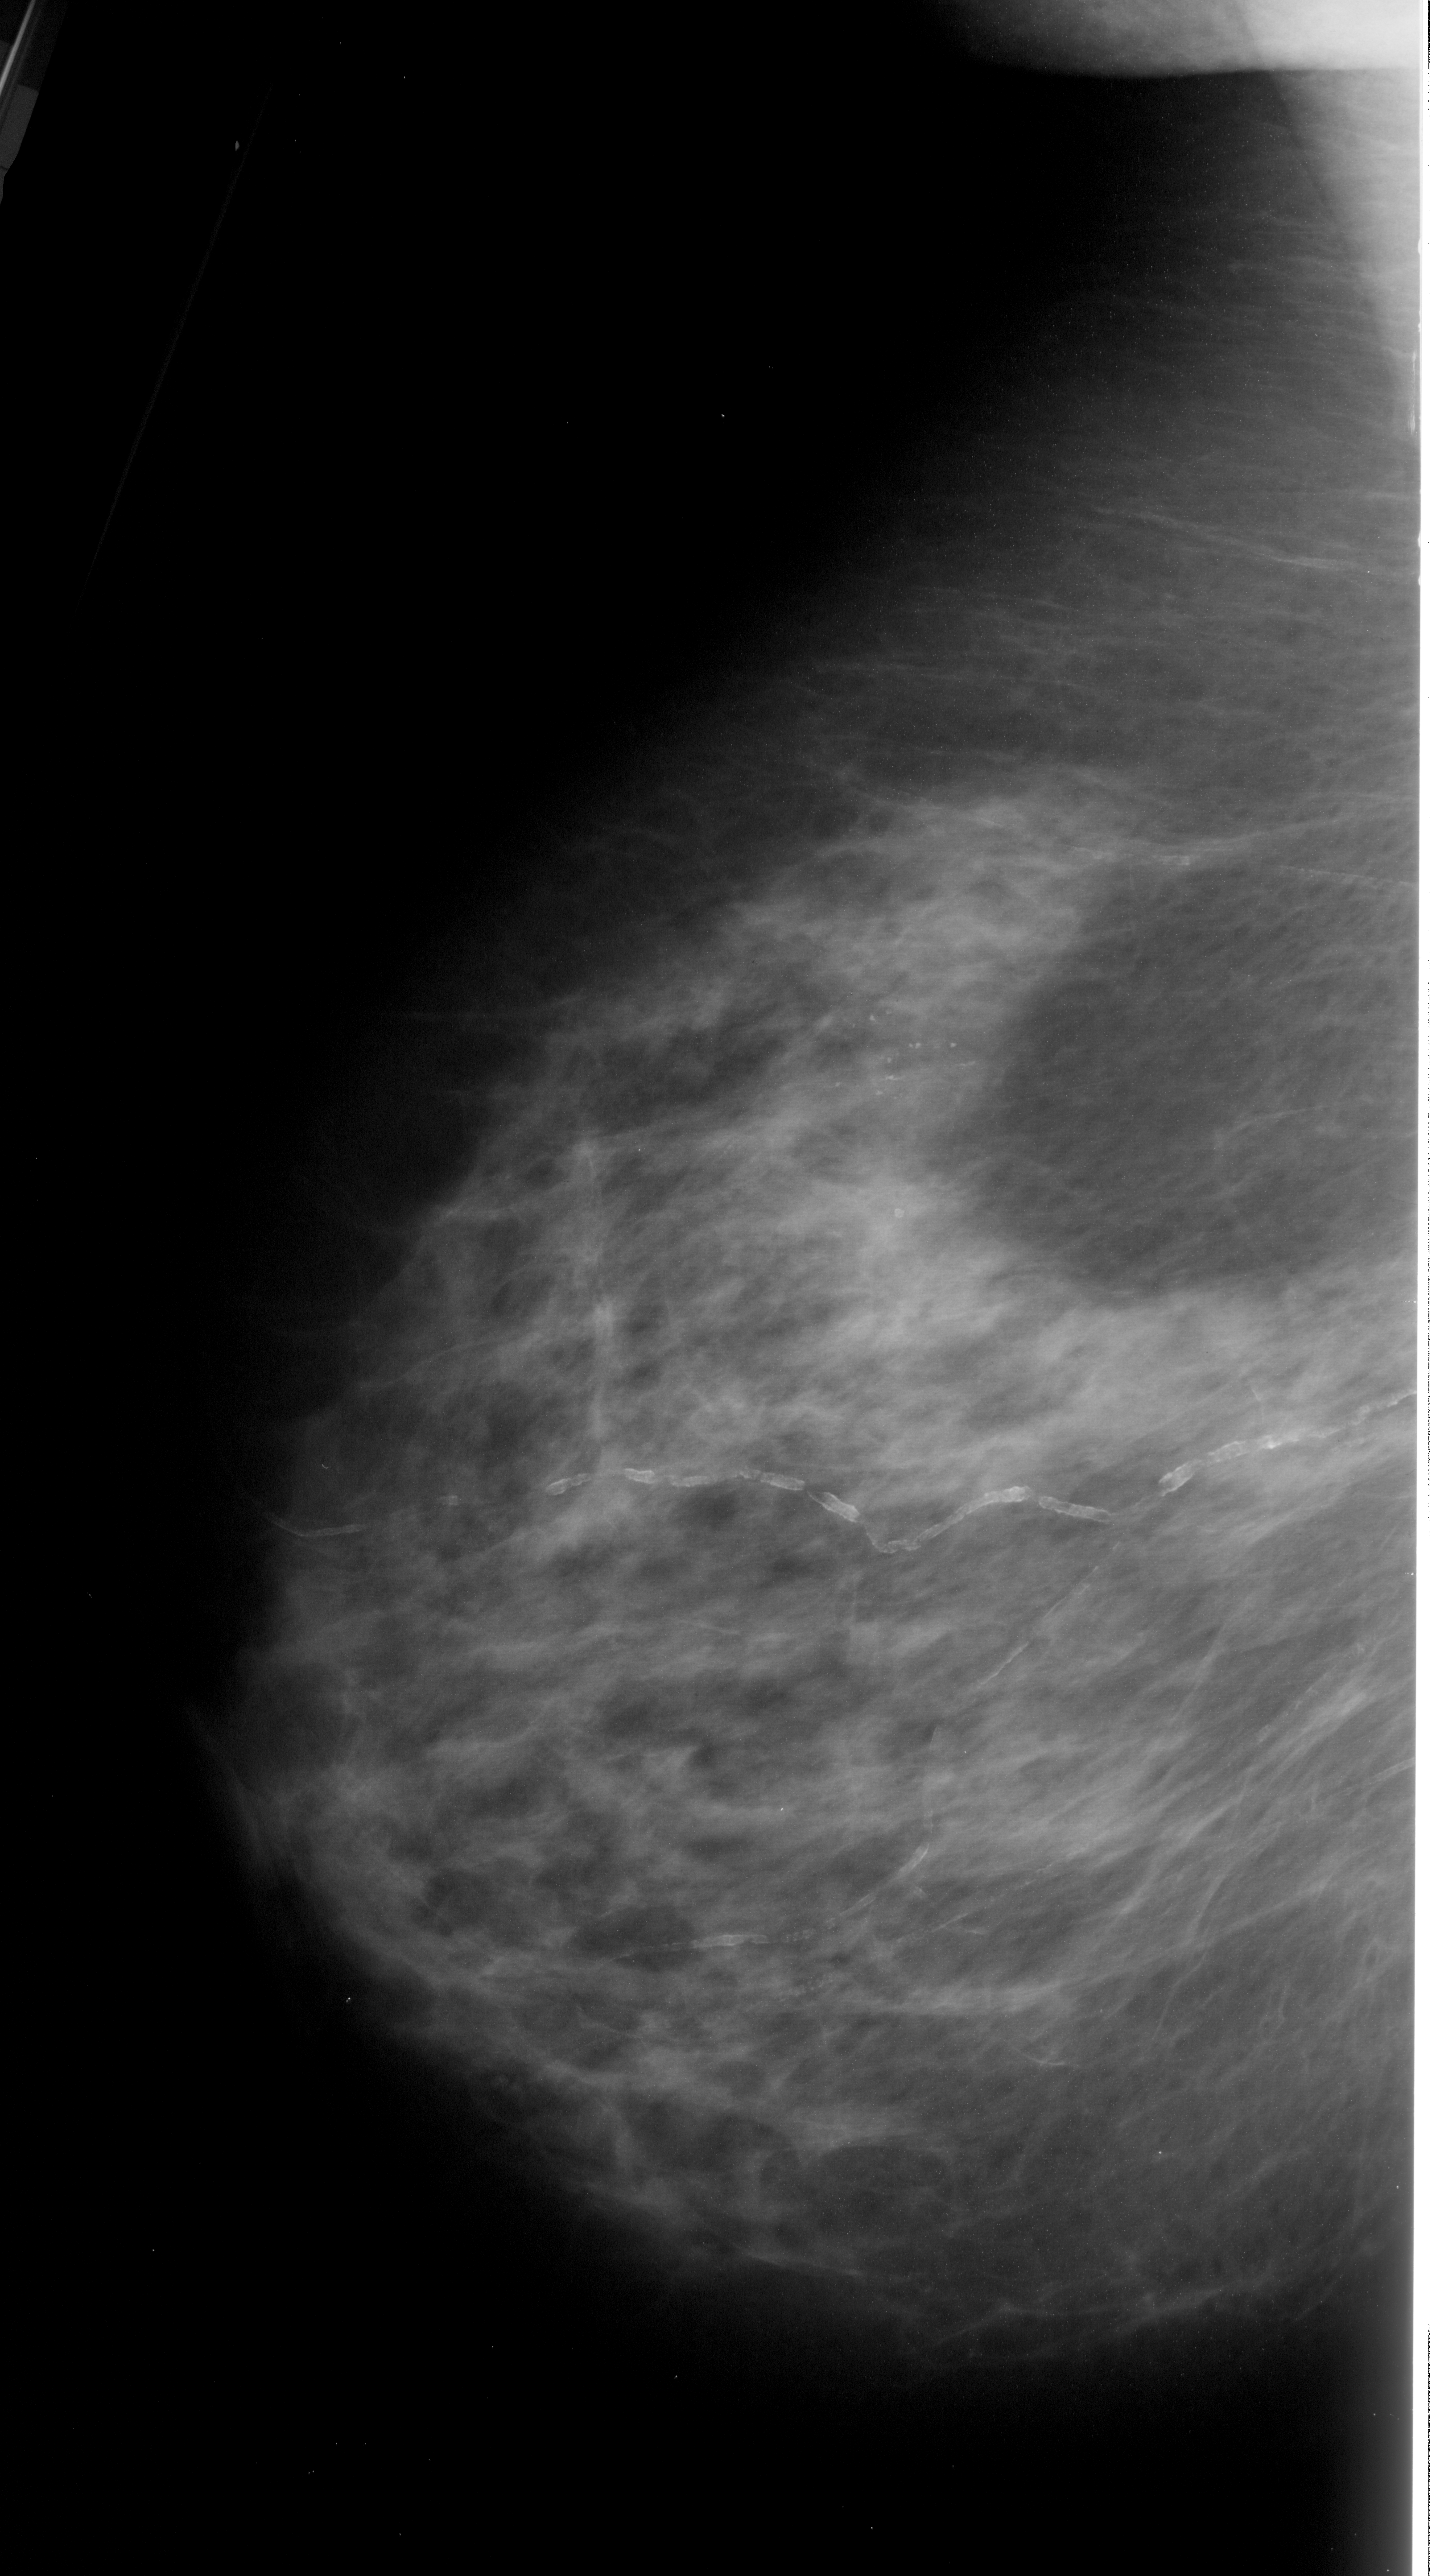
Digitized screen-film mammogram; left breast; mediolateral oblique (MLO) view; BI-RADS breast density category 3 (scale 1–4); 1432 × 2576 image matrix.
Marked abnormalities (boxes around the expert regions of interest):
- calcifications, morphology pleomorphic, distribution linear; BI-RADS assessment category 4; subtlety rating 3 on a 1 (subtle) to 5 (obvious) scale; pathology (as recorded): malignant: box from (x=703, y=1006) to (x=992, y=1186) px